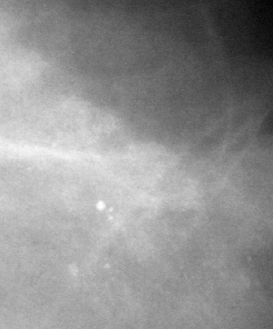
Region of interest cut from a scanned film mammogram (one marked finding); left breast; CC view.
Marked abnormality: calcifications, morphology pleomorphic, distribution clustered; BI-RADS assessment category 4; subtlety rating 3 on a 1 (subtle) to 5 (obvious) scale; pathology result (as recorded, not read from the image): benign.